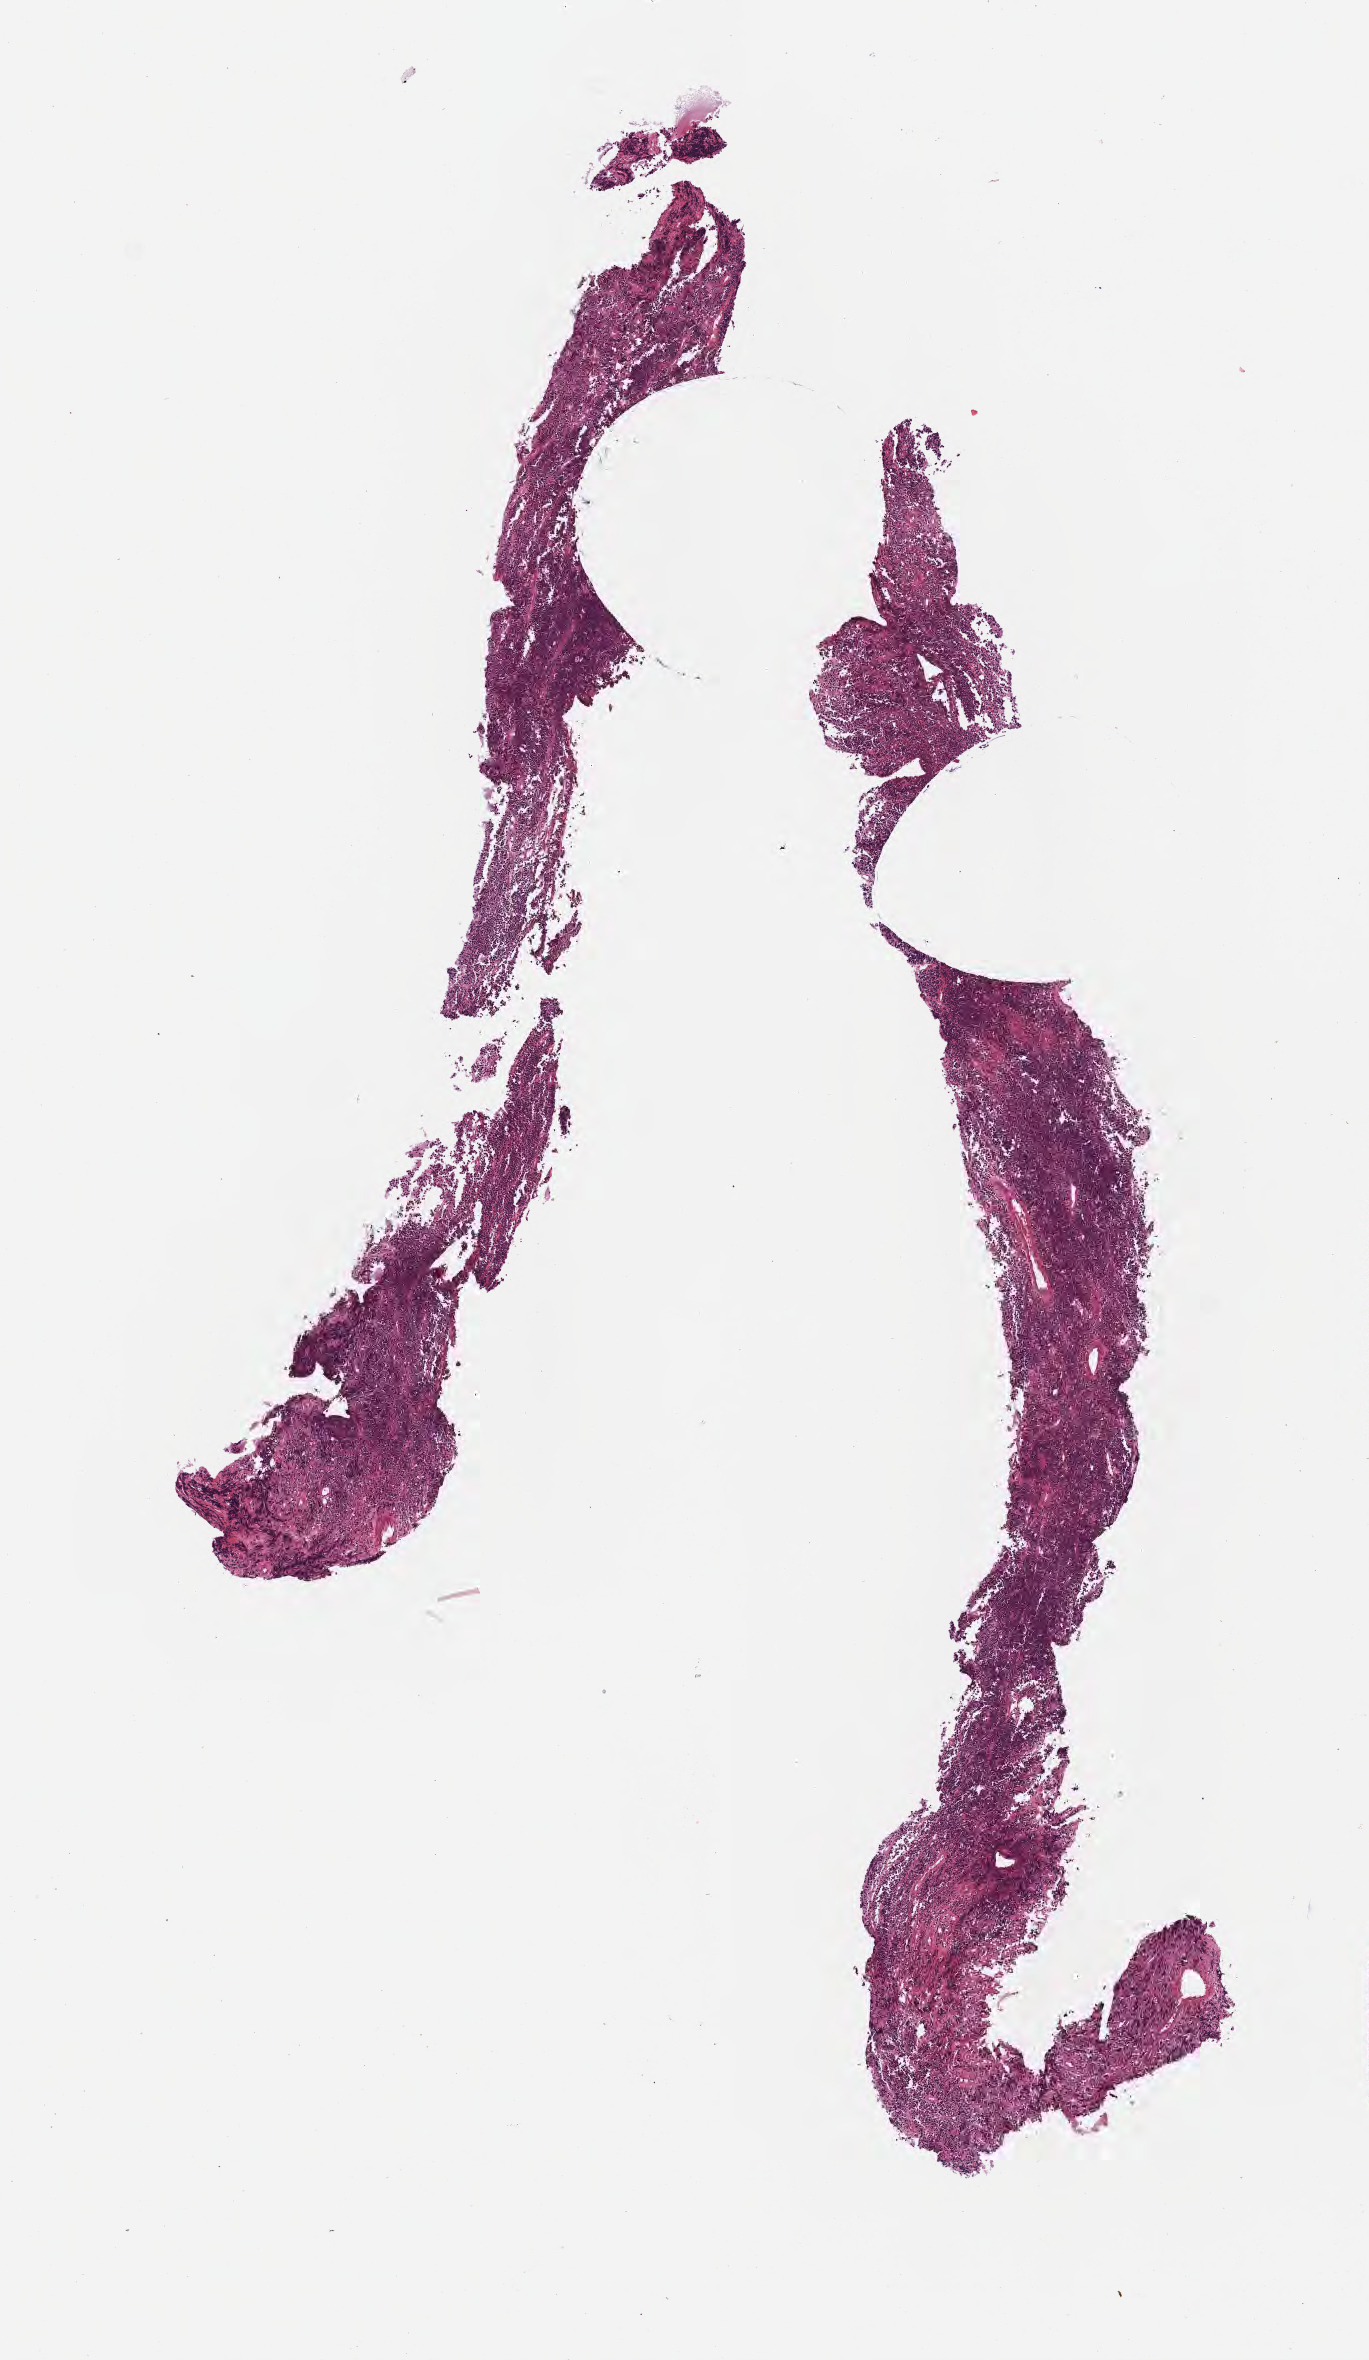
Digitized hematoxylin and eosin (H&E)-stained section — whole scanned area (about 5.5 x 9.5 mm) shown as a low-resolution overview; specimen: tumor tissue; site: spleen. Male, age 6 years at initial diagnosis.
* histologic diagnosis: Burkitt lymphoma, NOS